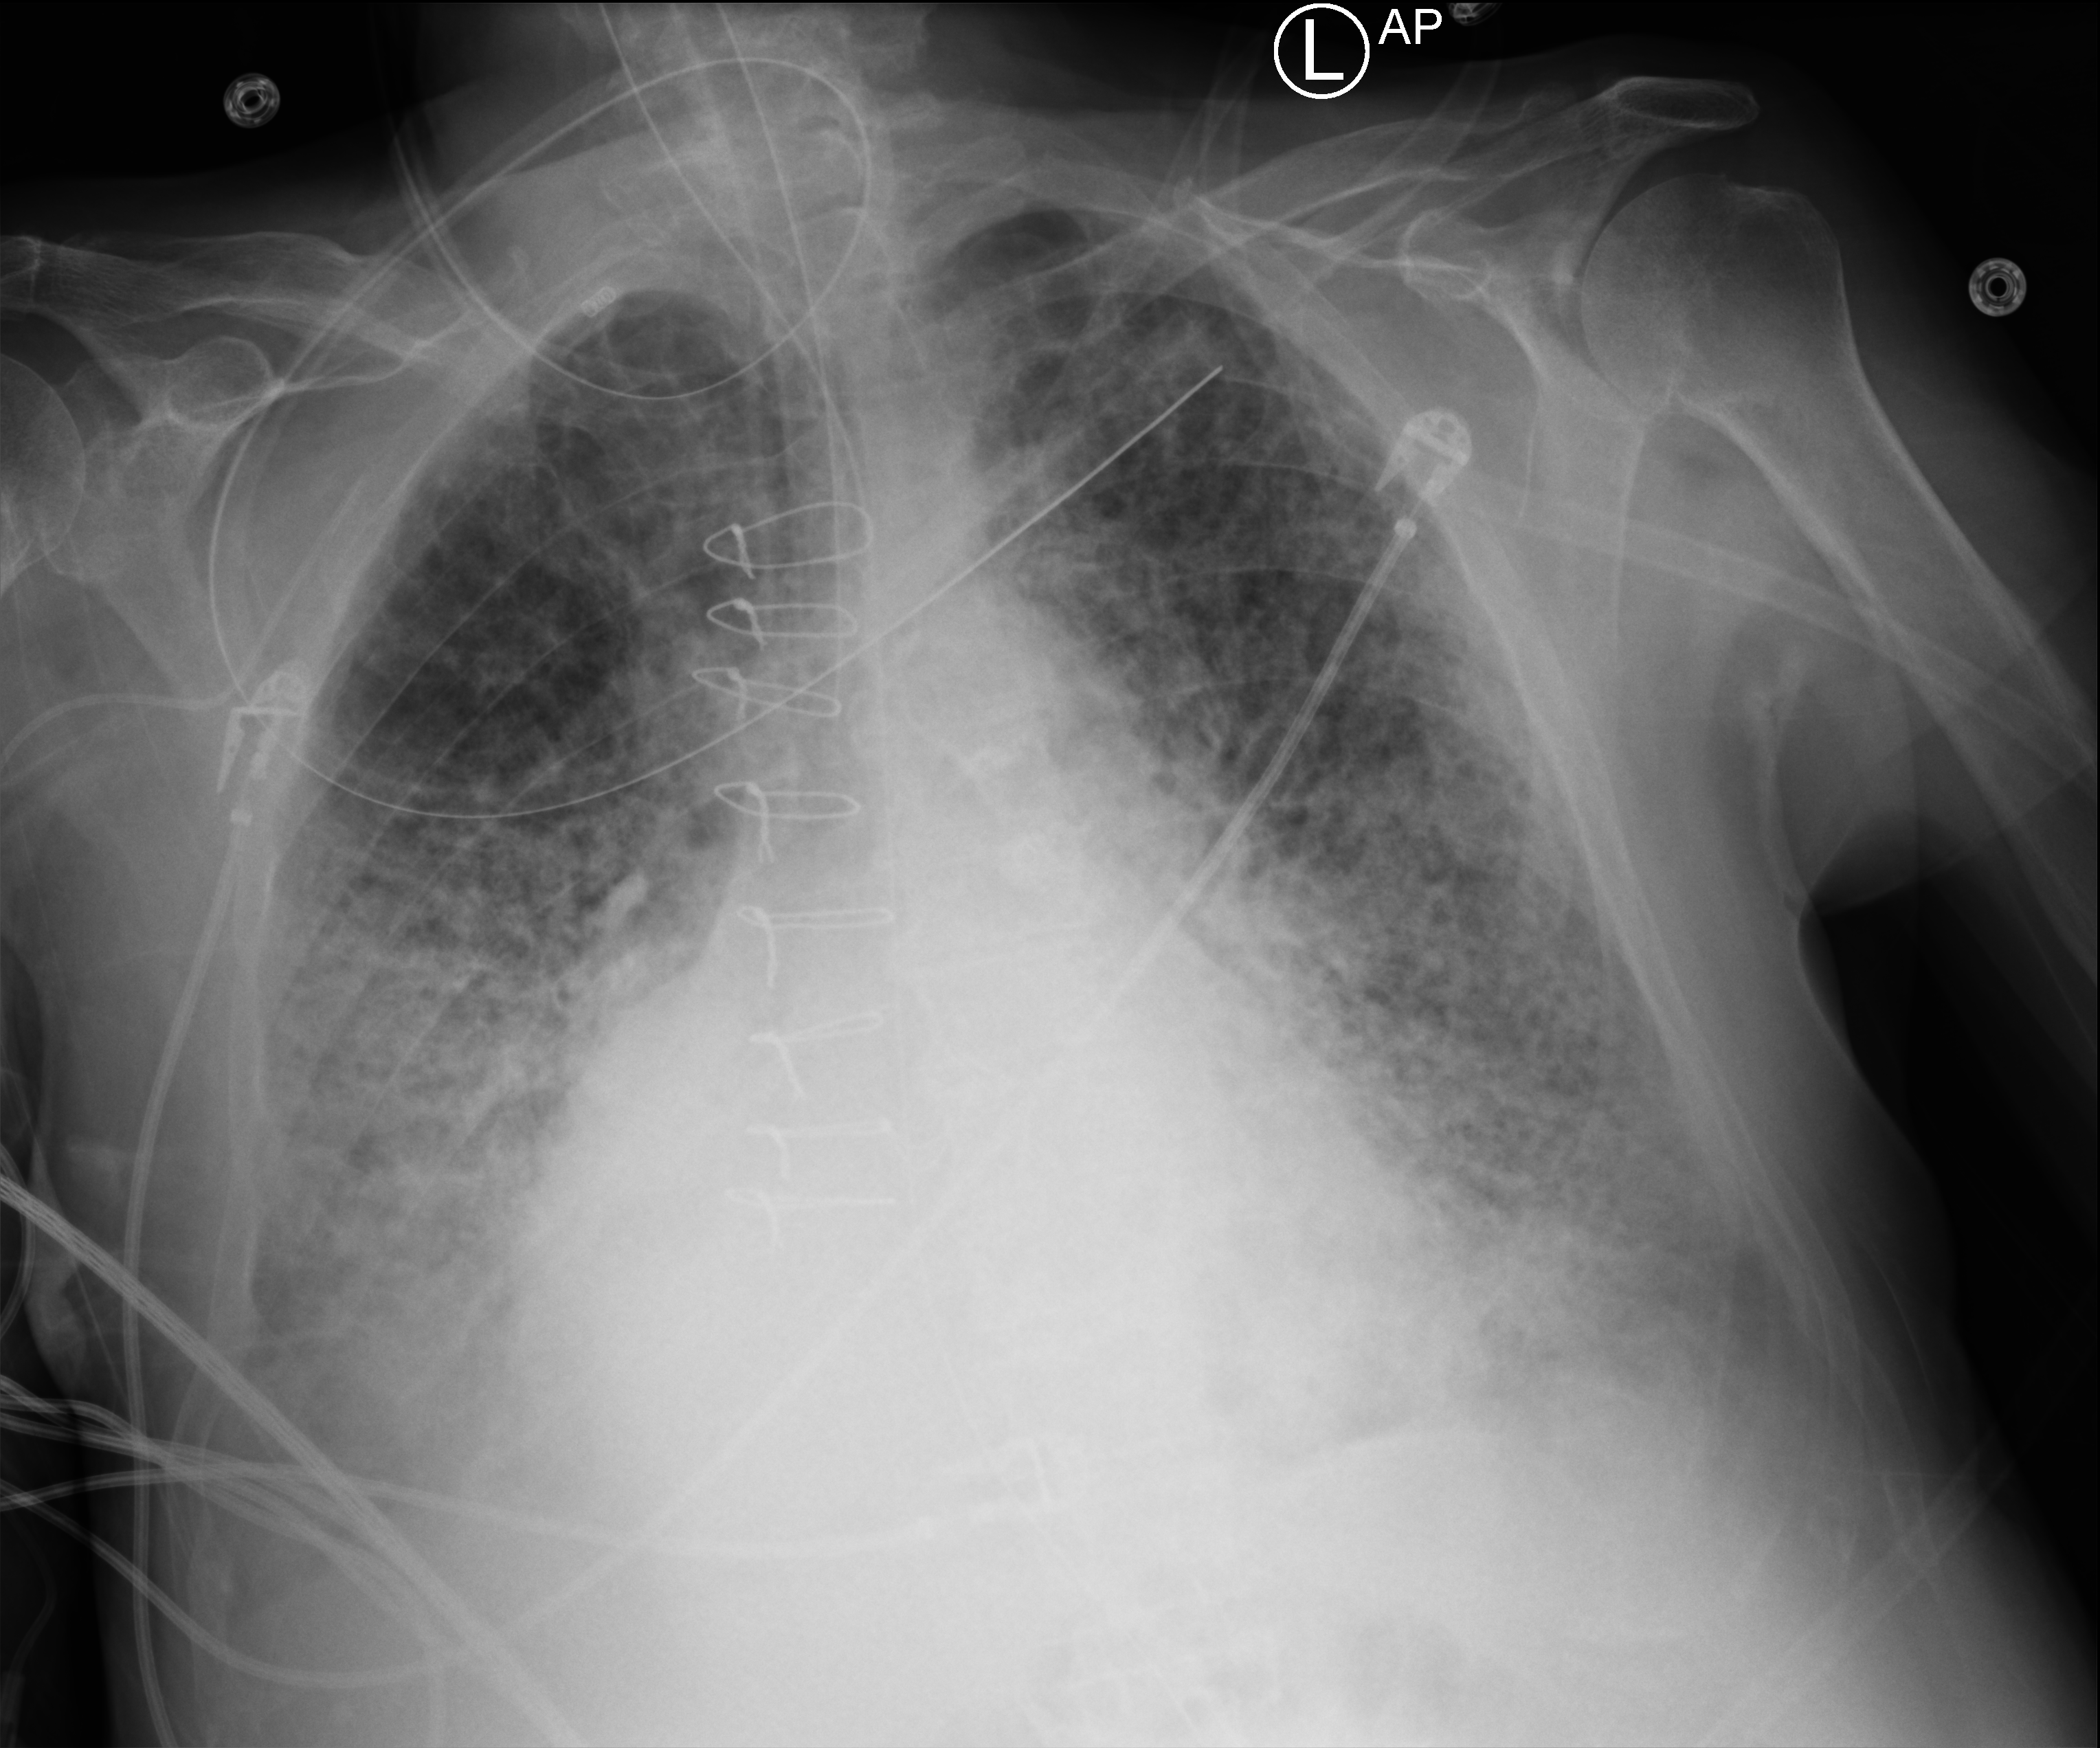
Portable chest radiograph; anteroposterior (AP) projection. Male patient hospitalised with COVID-19, age 75–90 years.
From the hospital-stay record, not from the radiograph (when in the stay this image was taken is not recorded): mechanically ventilated during this hospital stay: yes.